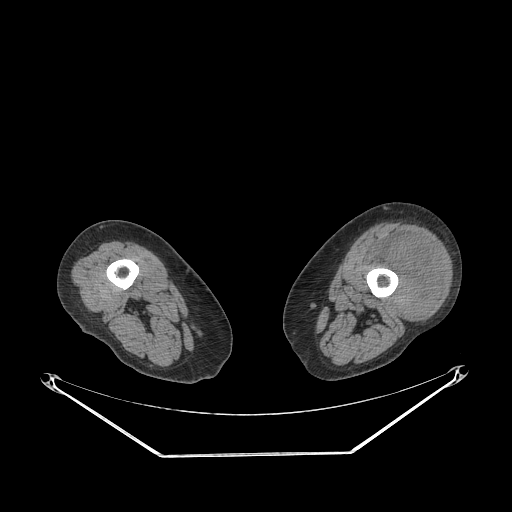
CT of an extremity soft-tissue mass (from a PET/CT study), one axial slice. Slice 207 of 267 in the series (ordered by position). Soft-tissue window (W 400 / L 40 HU). 3.75 mm slice thickness. 512 × 512 image matrix, field of view 500 × 500 mm. Female patient. From the clinical record (not read from this slice): histological type: undifferentiated – high grade; grade: high; site of the primary tumour: left thigh.
Outlined on this slice (expert contour drawn on MRI and transferred to this co-registered scan by the dataset authors):
- gross tumour volume including surrounding oedema: bounding box (x1, y1, x2, y2) in pixels: (368, 237, 442, 318)
- gross tumour volume (mass): (386, 237, 439, 318)